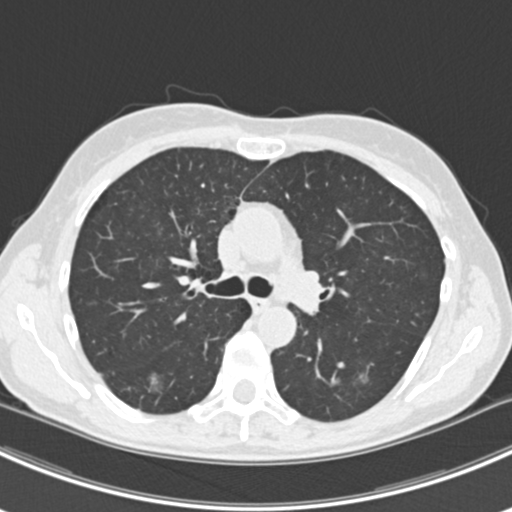
Chest CT (low-dose screening protocol), one axial image, baseline annual screen, lung window (W 1500 / L -600 HU), 2 mm slice thickness, slice 66 of 224 in the series. Female participant, aged 63 years at enrolment. Current smoker at enrolment.
2 lesions marked by an expert reader on this slice (largest first), bounding box (x1, y1, x2, y2) in pixels: (135, 364, 178, 402); (345, 362, 385, 394). The screening reader recorded 10 non-calcified nodules or masses ≥4 mm on this exam (right lower lobe, right lower lobe, left lower lobe, left lower lobe, right middle lobe, right lower lobe, left lower lobe, left upper lobe, right upper lobe, left upper lobe); which of them these boxes mark is not recorded. Official screen result: positive, change unspecified: nodule(s) >= 4 mm or enlarging nodule(s), mass(es), or other non-specific abnormalities suspicious for lung cancer. Lung cancer was diagnosed 751 days after this screen (after the third annual screen): bronchiolo-alveolar adenocarcinoma, NOS, right upper lobe, right middle lobe, right lower lobe, left upper lobe, left lower lobe, moderately differentiated (G2), stage IV (AJCC 6th edition).